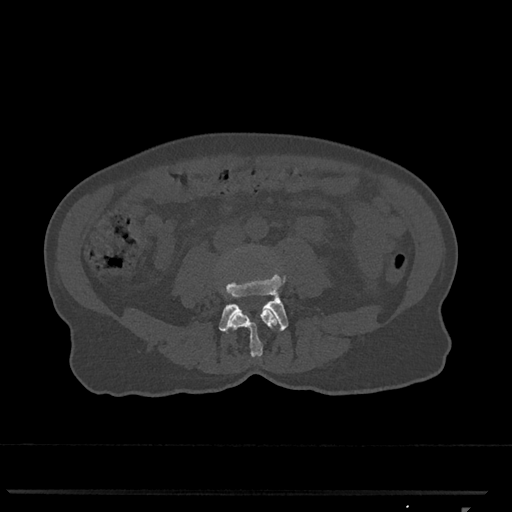
CT including the spine, one axial slice. Position 236 of 793 along the scan axis. Reconstruction kernel Br40s/3. 120 kVp. Bone window (W 1800 / L 400 HU). 512 × 512 image matrix, field of view 380 × 380 mm. Patient: female, 62 years. Case-level facts recorded for this patient, not image findings: primary cancer: renal.
Structures marked on this image (semi-automatically segmented with operator editing):
- L3 vertebra: bounding box (x1, y1, x2, y2) in pixels: (230, 309, 278, 357)
- L4 vertebra: (219, 274, 289, 333)